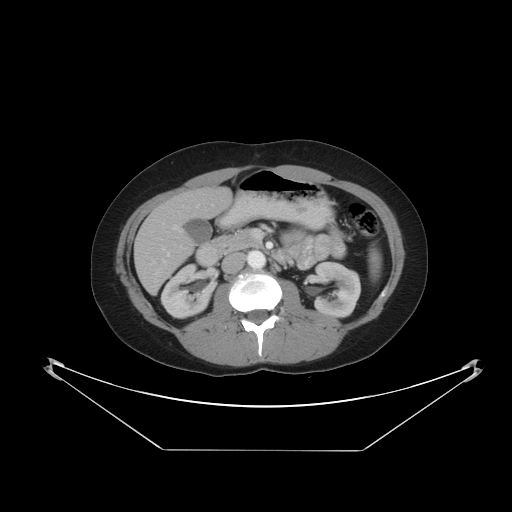
Contrast-enhanced abdominal CT, one axial slice; position 19 of 48 along the scan axis; 120 kVp; intravenous contrast given; soft-tissue window (W 400 / L 40 HU); 5 mm slice thickness; 512 × 512 image matrix, field of view 482 × 482 mm. Female patient, age 38 years. Case-level facts recorded for this patient, not image findings: diagnosis: colorectal cancer liver metastases, imaged before liver resection; multiple liver metastases: yes; largest metastasis: 2.5 cm; disease in both lobes: no.
Outlined on this slice (expert manual segmentation):
- hepatic veins: bounding box (x1, y1, x2, y2) in pixels: (173, 225, 181, 232)
- liver: (136, 188, 232, 292)
- planned liver remnant (the part of the liver to remain after resection): (170, 188, 232, 220)
- portal vein (with intrahepatic branches): (163, 204, 213, 263)